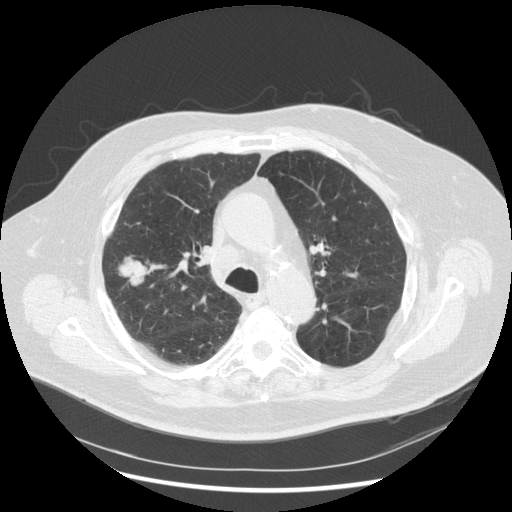
Low-dose screening chest CT, one axial slice. Slice 190 of 263 in the series (ordered by position). Reconstruction kernel STANDARD. 120 kVp. Lung window (W 1500 / L -600 HU). 2.5 mm slice thickness. 512 × 512 image matrix, field of view 400 × 400 mm.
Structures marked on this image (outlined manually by an expert reader):
- lesion 1 (tumor, upper lobe of right lung): box from (x=119, y=258) to (x=147, y=285) px